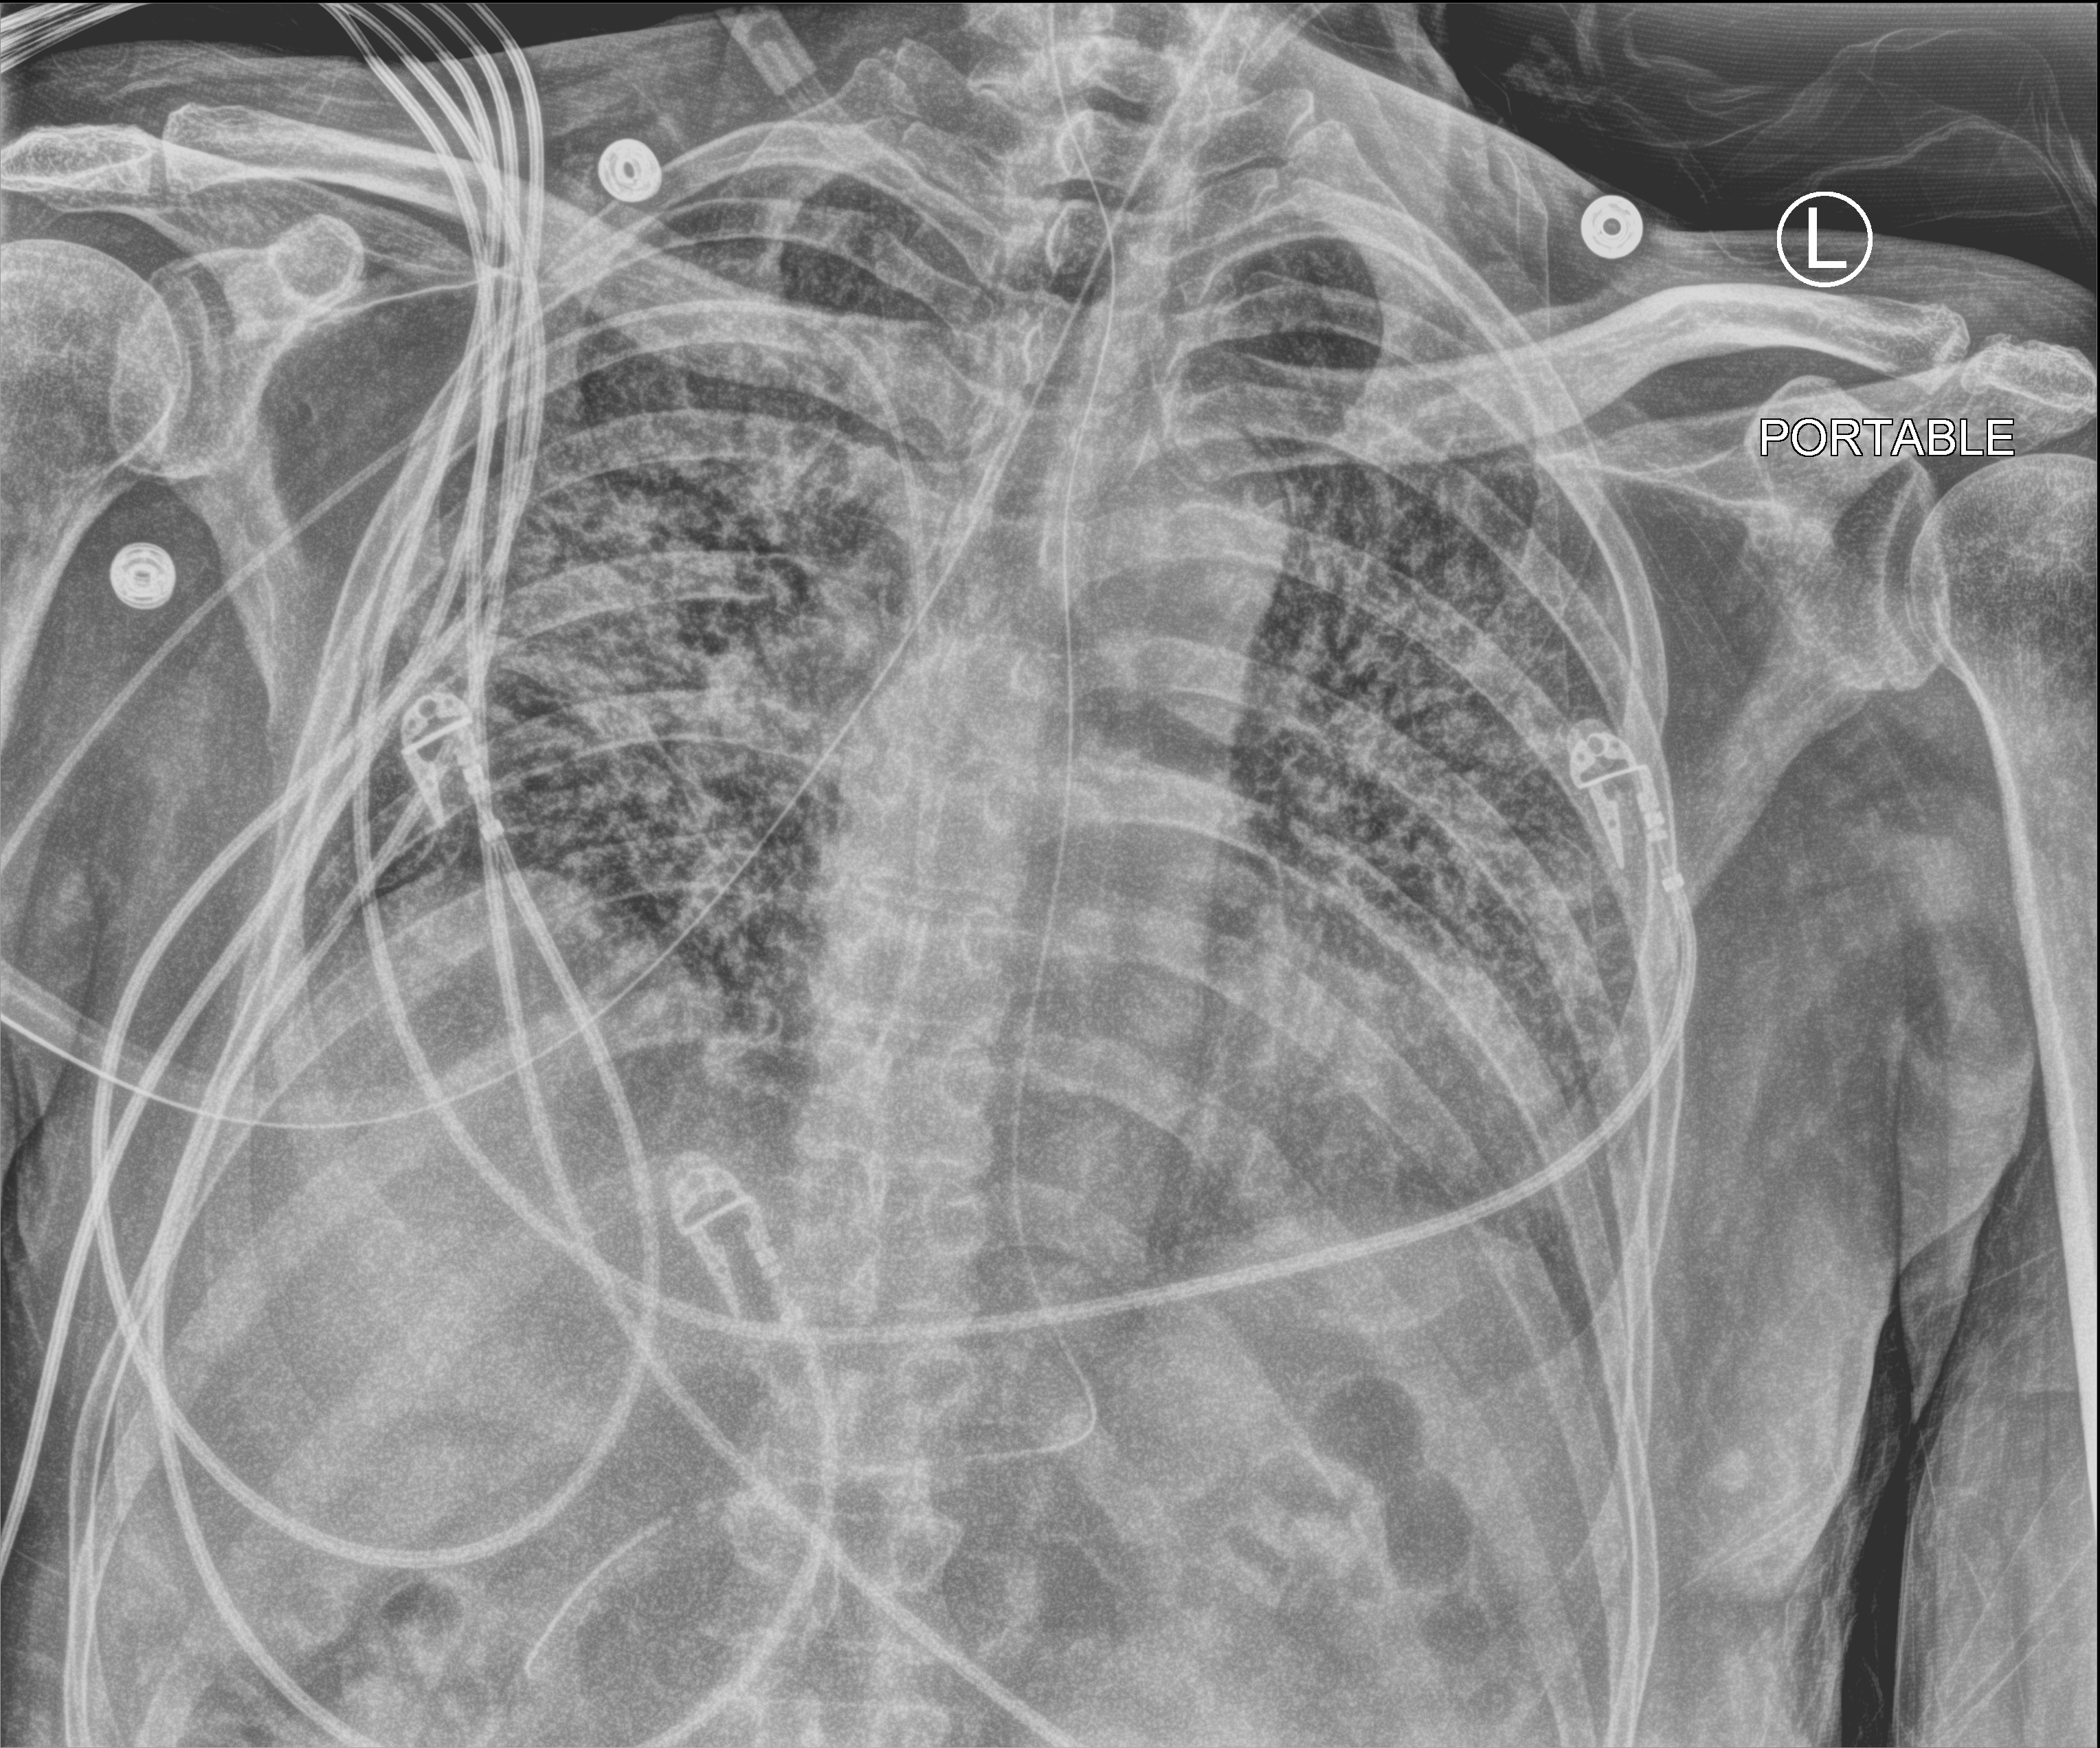
Chest X-ray (portable); anteroposterior (AP) projection. Patient hospitalised with COVID-19; male, aged 60–74 years.
From the hospital-stay record, not from the radiograph (when in the stay this image was taken is not recorded): mechanically ventilated during this hospital stay: yes; length of hospital stay: 28 days; hypertension (admission record): yes.